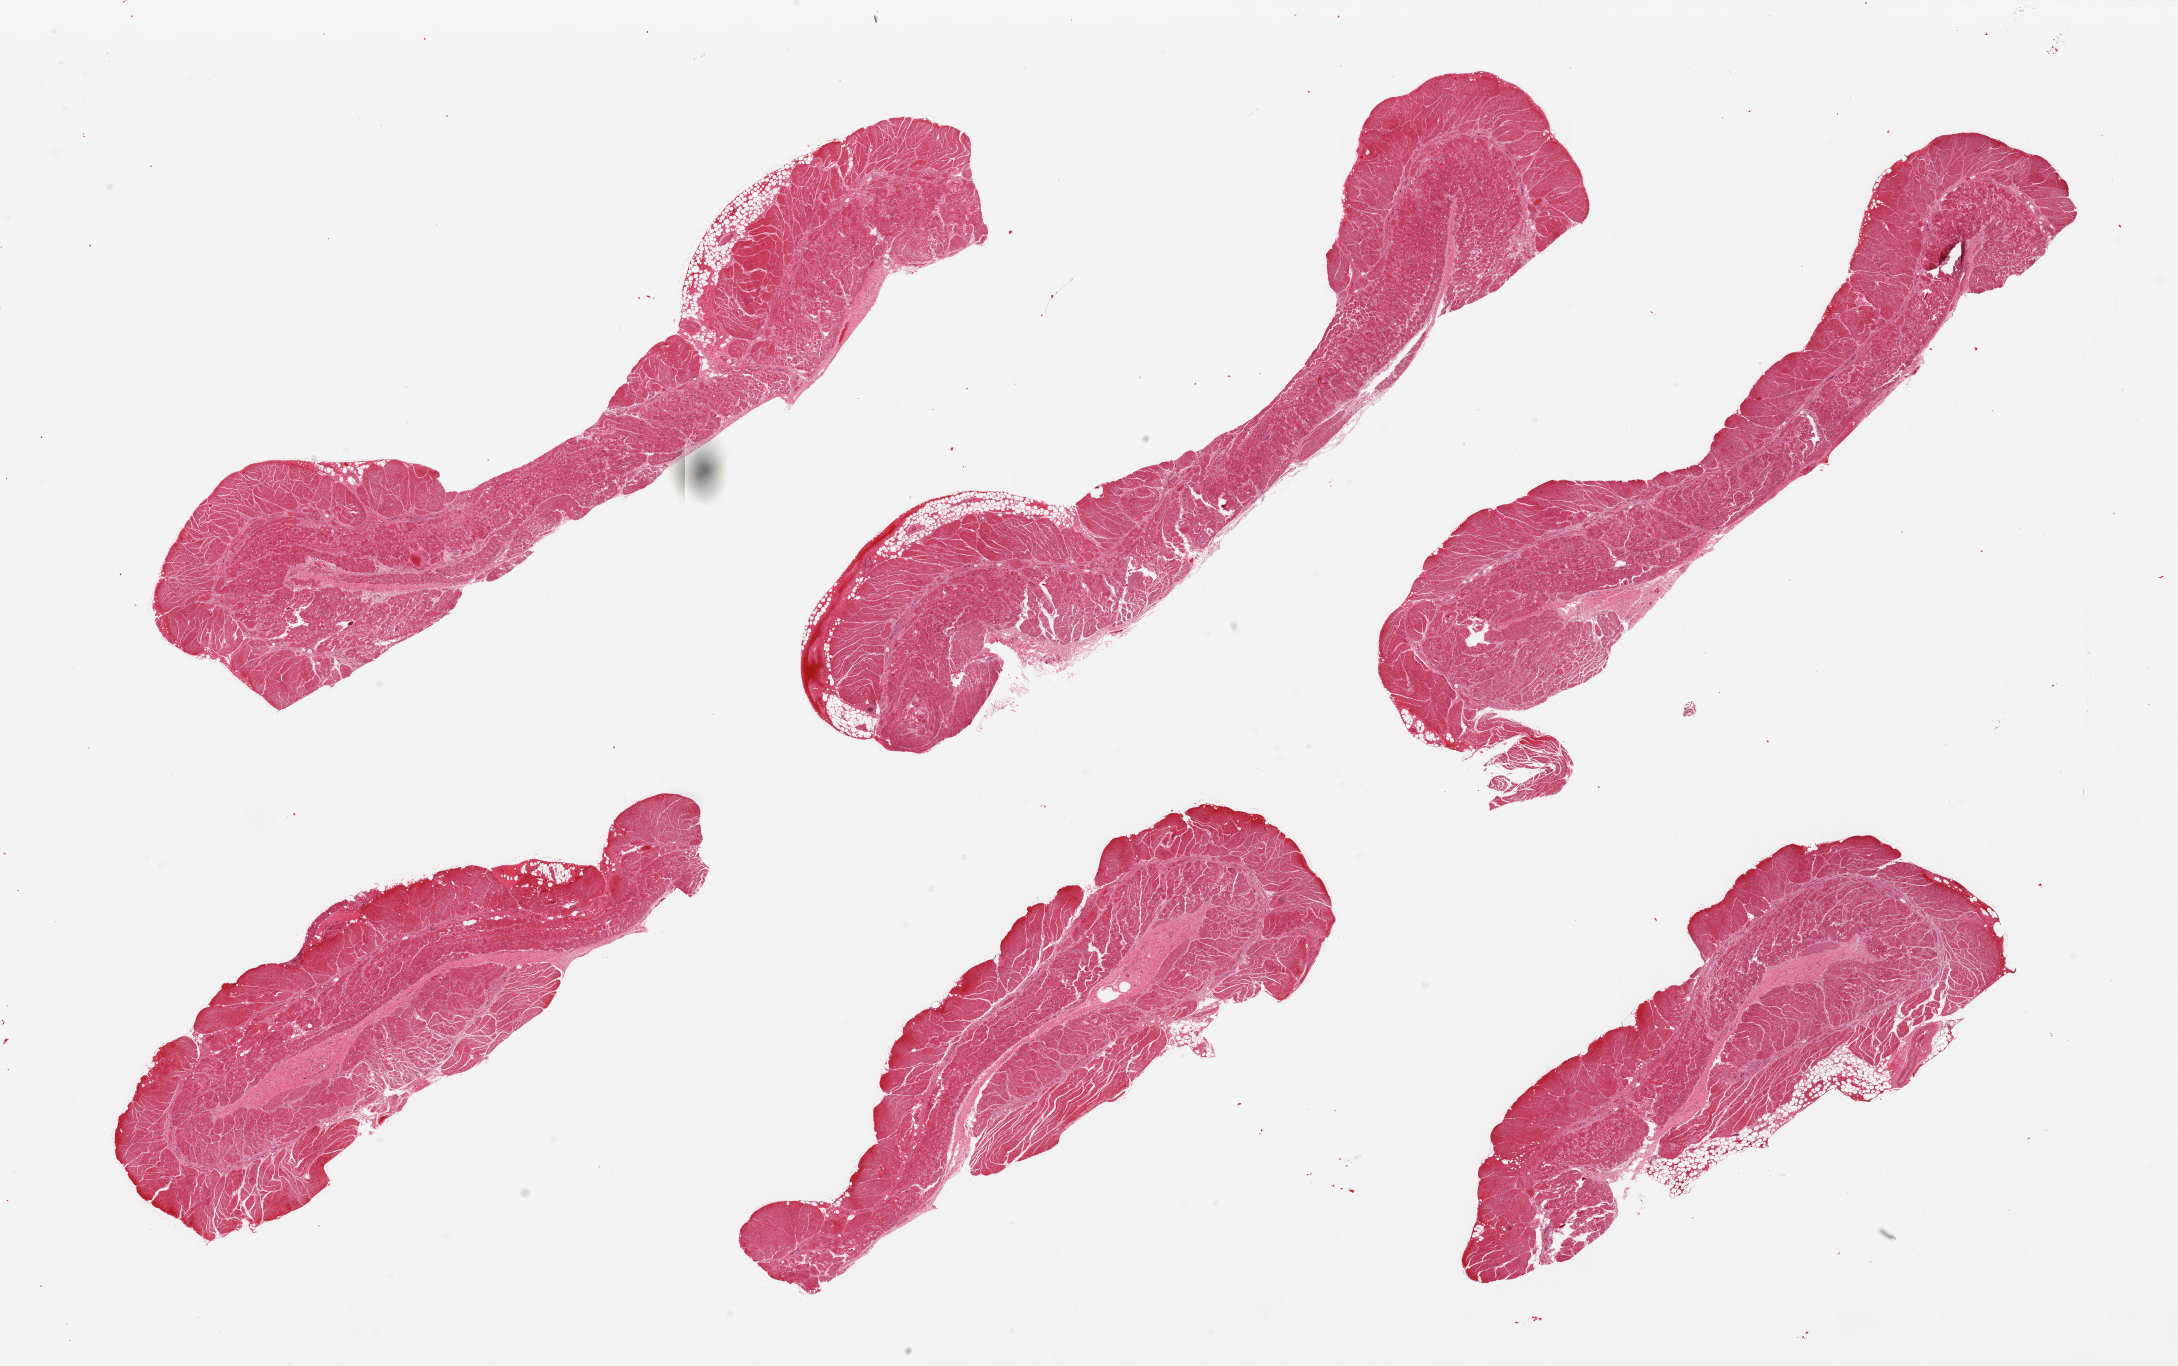
Whole-slide image, hematoxylin and eosin (H&E) stain, brightfield — low-resolution overview of the scanned area, about 34.5 x 21.6 mm (acquisition: 20x scan). PAXgene-fixed paraffin-embedded (PFPE) section. Target tissue: esophageal muscle. Tissue donor sample. Male donor.
* pathologist's review note for this sample: 6 pieces; well dissected muscle with limited amount of extraneous fat